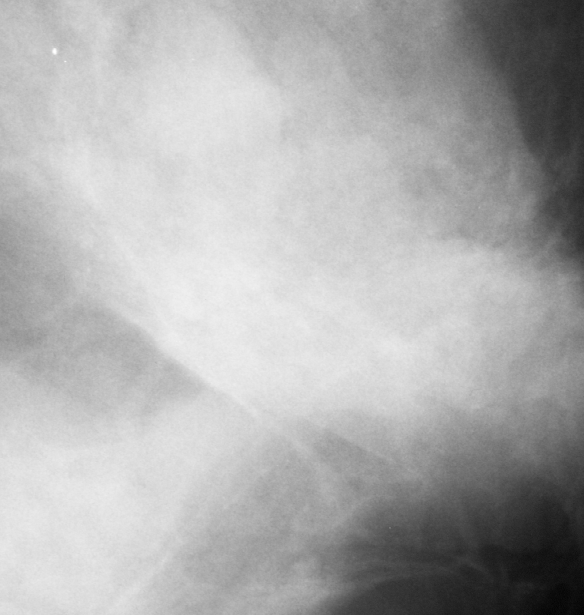
Region of interest cut from a scanned film mammogram (one marked finding); left breast; MLO view; BI-RADS breast density category 3 (scale 1–4).
- Marked abnormality: mass, shape architectural distortion, margins ill defined; BI-RADS assessment category 3; benign without callback (not worked up further).